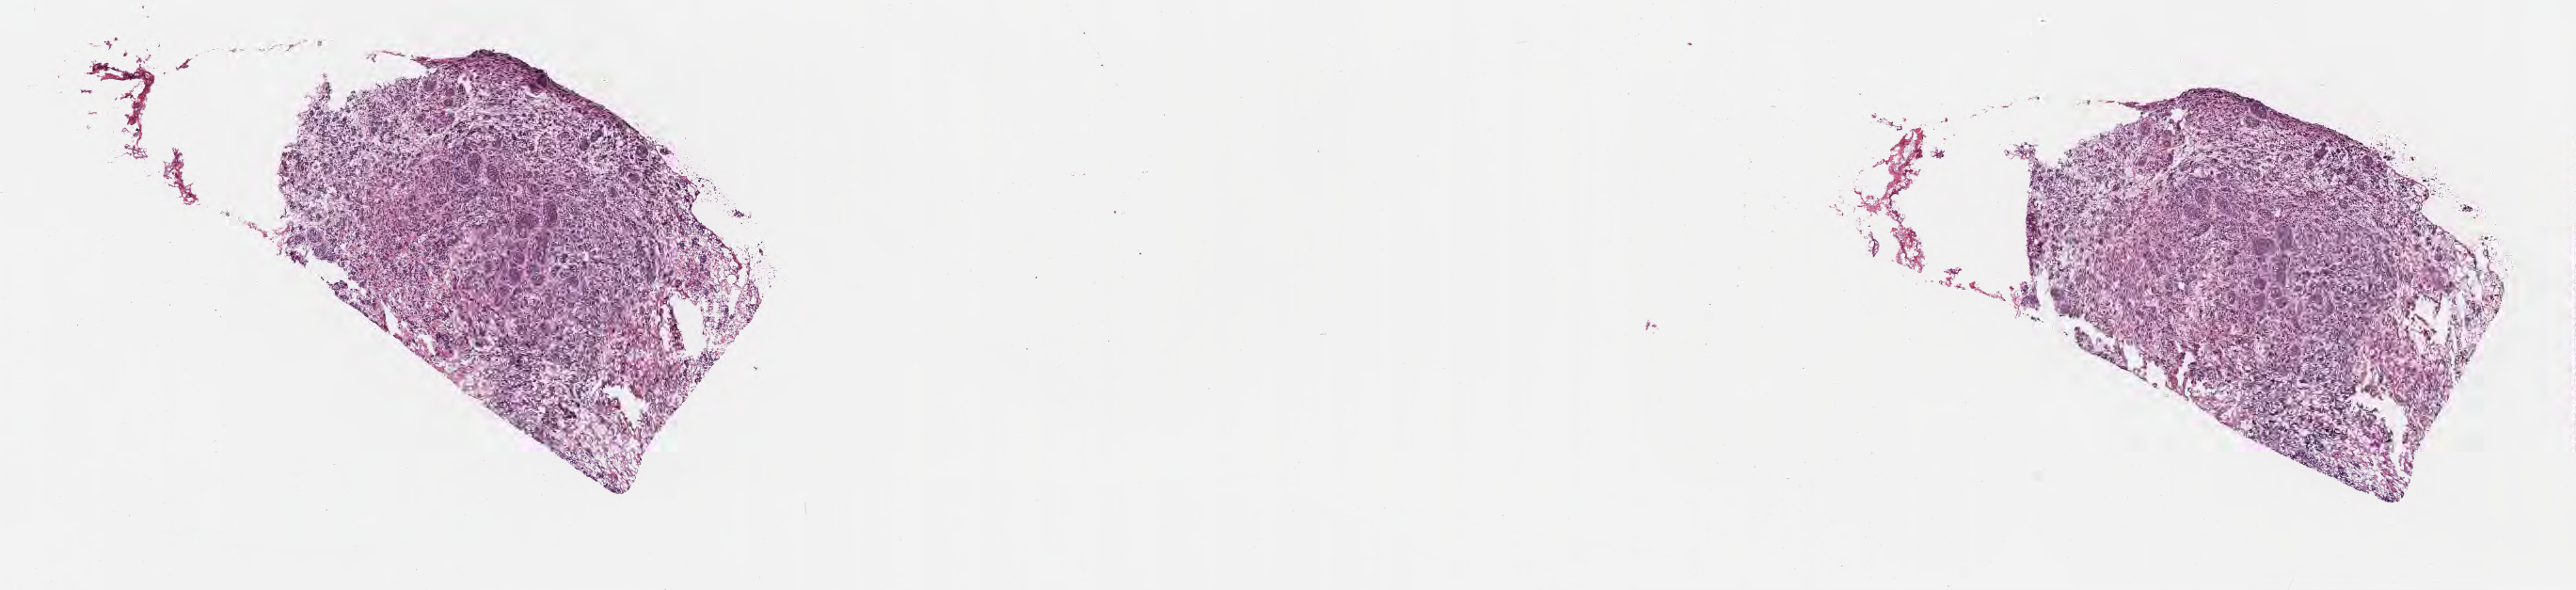
Digitized hematoxylin and eosin (H&E)-stained section — whole scanned area (about 22.1 x 5.1 mm) shown as a low-resolution overview. Frozen section (tissue freezing medium). Specimen: metastatic tumor tissue, resected from lymph node. Female patient; age at initial diagnosis 39 years. Pathologist review of this section (percent, as recorded): tumor cells 45%, tumor nuclei 92%, stromal cells 55%, necrosis 0%, normal cells 0%. Inflammatory infiltration, as recorded: lymphocyte infiltration 5%, monocyte infiltration 0%, neutrophil infiltration 0%.
* section: top of the tissue portion
* patient diagnosis (primary): Atypical carcinoid tumor